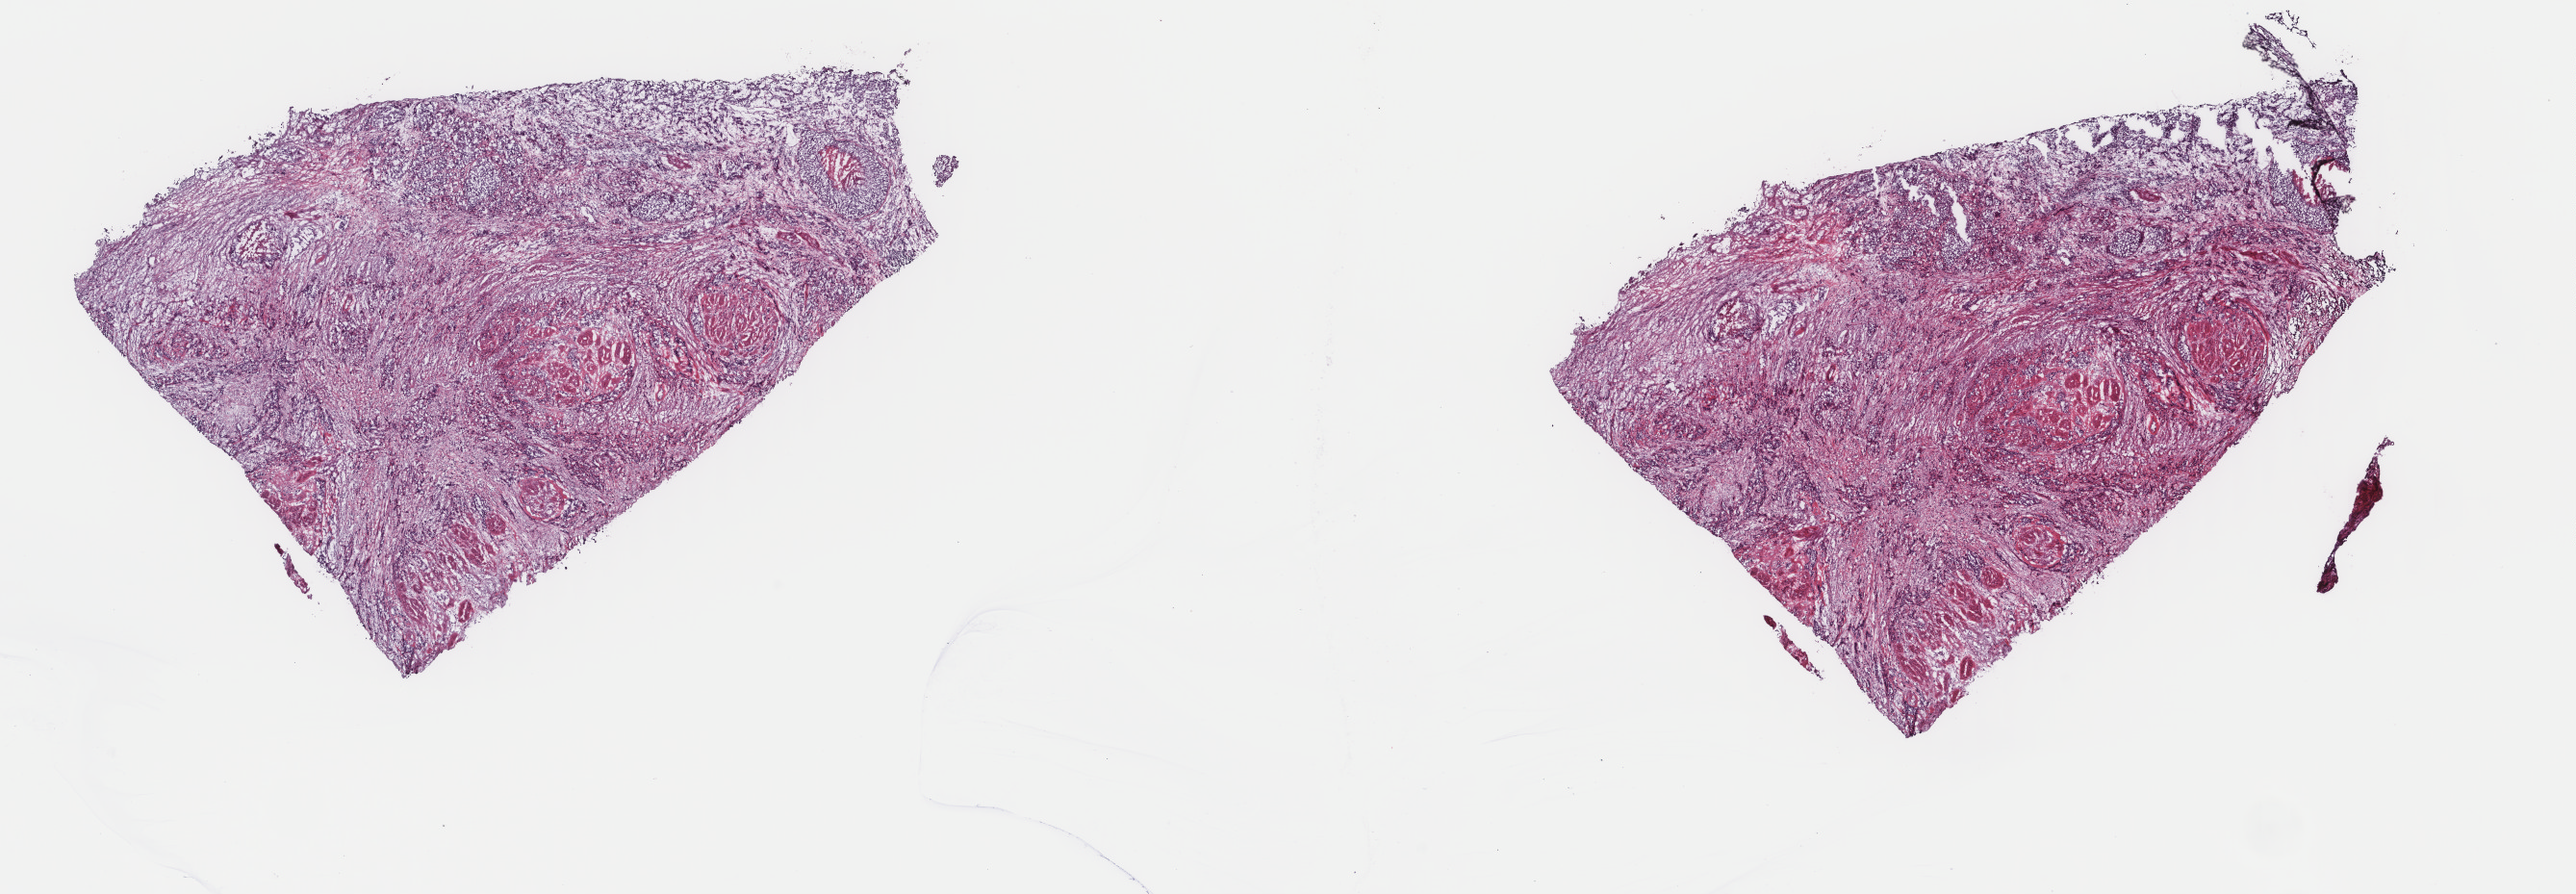
H&E whole-slide image, shown as a low-resolution overview of the whole scanned area (about 21.2 x 7.4 mm, acquisition: 40x scan); frozen section; sample: primary tumour, bladder. Male patient; age at initial diagnosis 87 years. Histologic grade: high grade. Composition of this section per pathologist review: tumour cells 80%, tumour nuclei 75%, normal cells 10%, stromal cells 10%, necrosis 0%. Inflammatory infiltration, as recorded: lymphocyte infiltration 2%, monocyte infiltration 0%, neutrophil infiltration 0%.
Diagnosis: Transitional cell carcinoma (lateral wall of bladder). AJCC pathologic stage: IV (6th edition). TNM: T3 N2 M0.